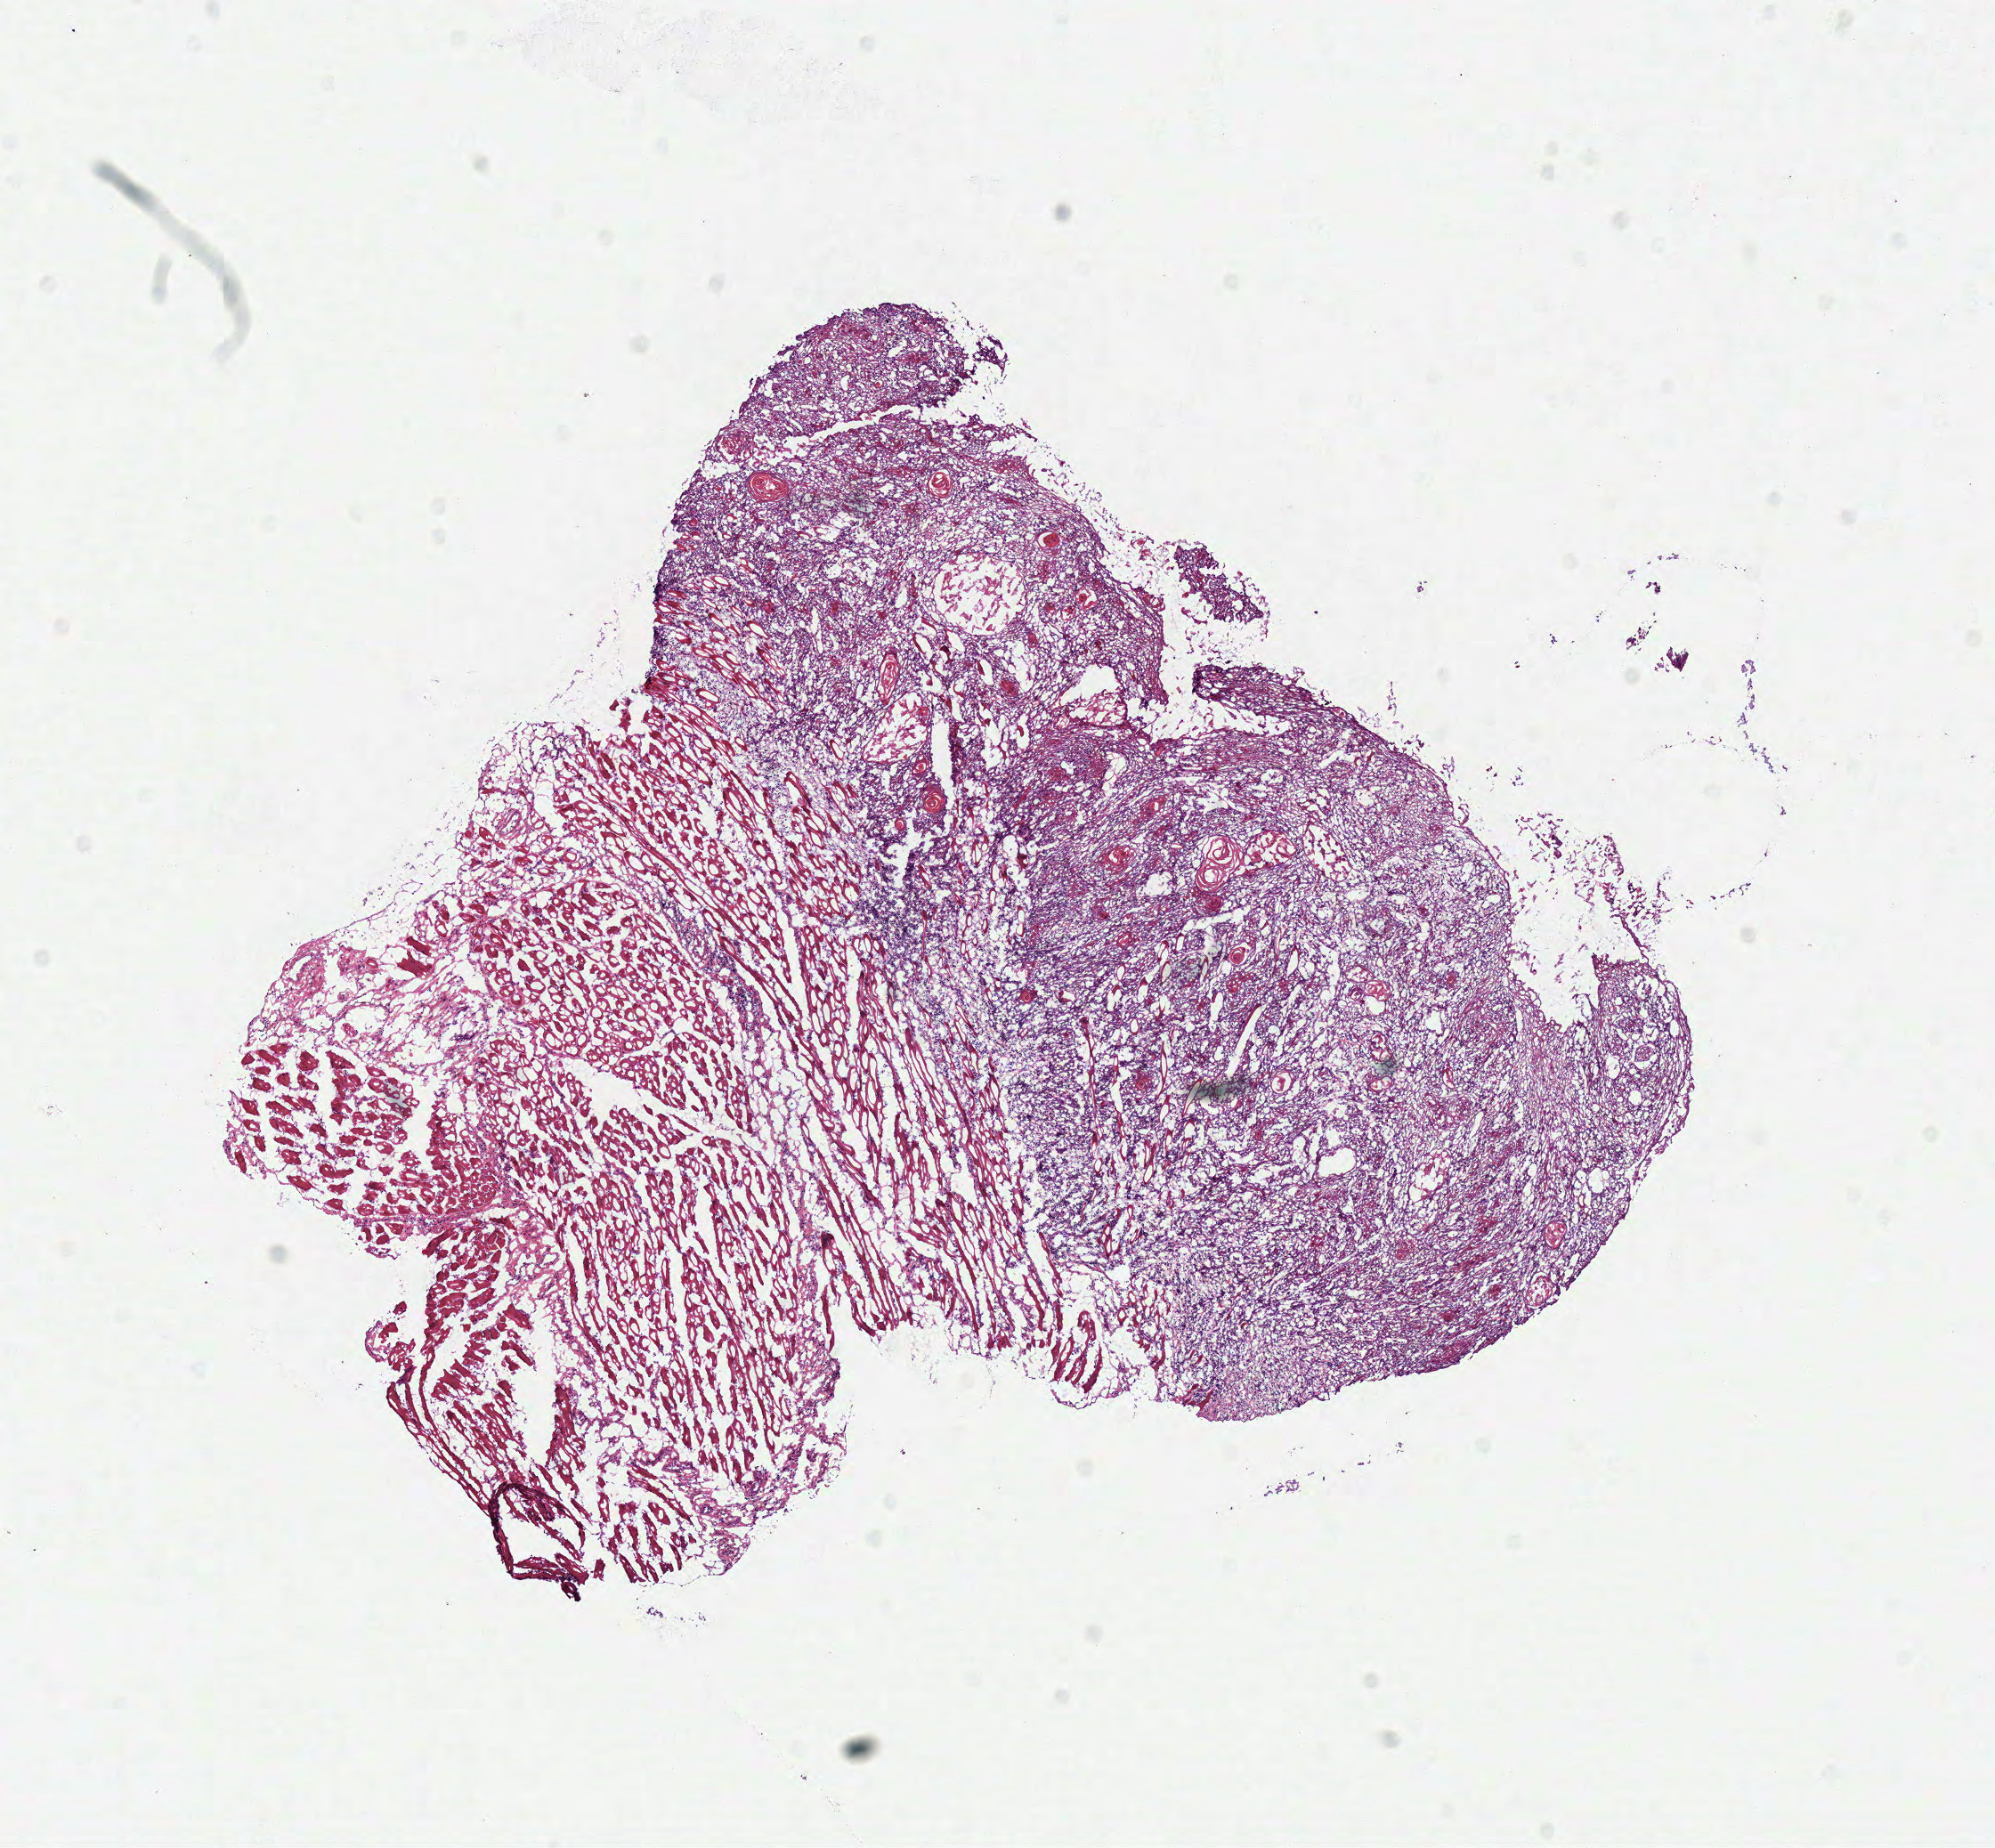
Digitized H&E-stained tissue section (whole slide) — a low-resolution overview of the entire scanned area, about 8.8 x 8.2 mm (from a 40x scan). Frozen section from the top of the tissue portion. Head and neck, primary tumour sample. Patient: female, age at initial diagnosis 52 years. Histologic grade: G2 (moderately differentiated). Composition of this section per pathologist review: tumour cells 55%, tumour nuclei 80%, normal cells 40%, stromal cells 5%, necrosis 0%.
- laterality: right
- diagnosis: Squamous cell carcinoma, NOS (tongue, NOS)
- lymph nodes positive (case pathology): 0 of 19 examined